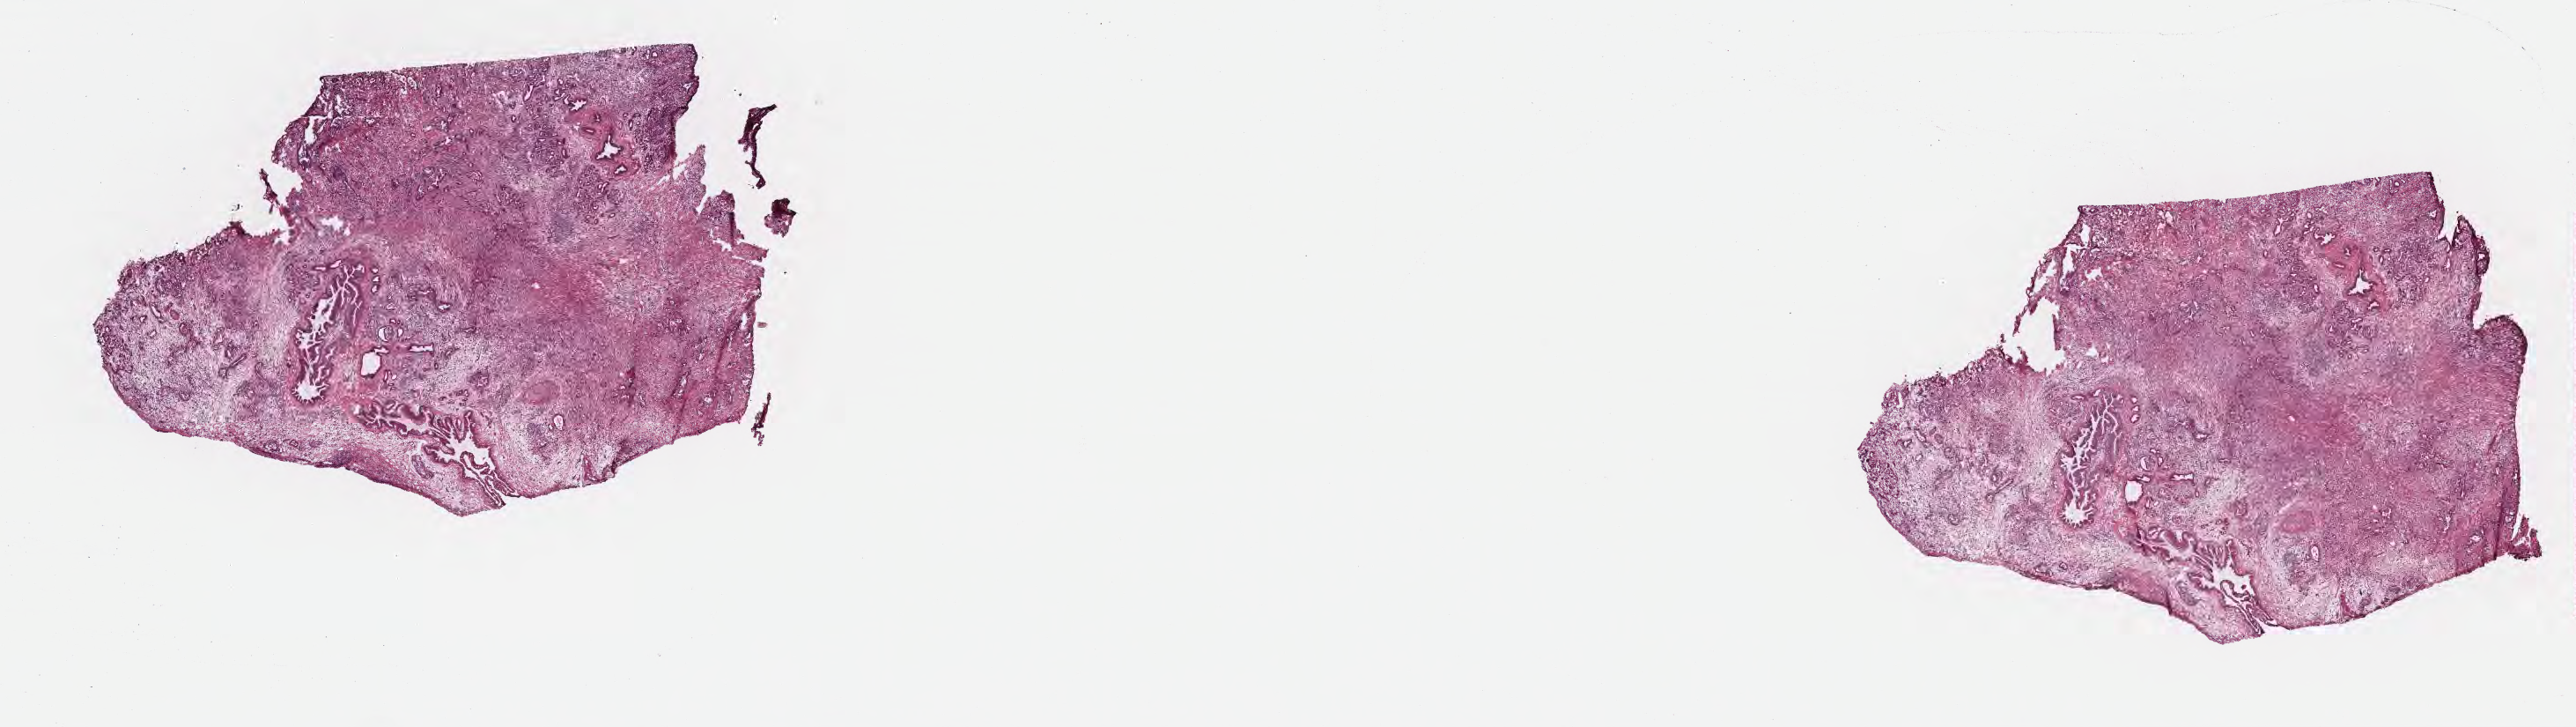
Digitized hematoxylin and eosin (H&E)-stained section — a low-resolution overview of the entire scanned area, about 23.7 x 6.7 mm; frozen section; specimen: primary tumor; site: head of pancreas. Female patient; age at initial diagnosis 60 years. Tumor grade: G2 (moderately differentiated). Composition of this section per pathologist review: tumor cells 40%, tumor nuclei 50%, stromal cells 60%, necrosis 0%, normal cells 0%. Infiltration values recorded for this section: lymphocyte infiltration 0%, monocyte infiltration 0%, neutrophil infiltration 0%.
• diagnosis: Infiltrating duct carcinoma, NOS
• AJCC pathologic stage: Stage III